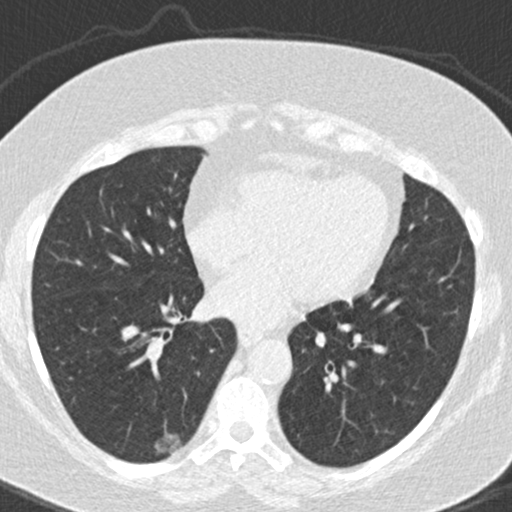
Low-dose screening chest CT, axial slice; baseline annual screen; lung window (W 1500 / L -600 HU); 2 mm slice thickness; standard (soft-tissue) reconstruction kernel (B30f); 120 kVp; slice 106 of 177 in the series; 512 × 512 image matrix, field of view 300 × 300 mm. Female participant, aged 63 years at enrolment. Former smoker at enrolment.
• Lesion marked by an expert reader, bounding box [x1, y1, x2, y2] px = [147, 425, 188, 462].
• Reader record for this screening exam (exam-level; its link to the box is not recorded): non-calcified nodule or mass ≥4 mm, right lower lobe, 16 × 10 mm, poorly defined margins, ground glass attenuation.
• Official screen result: positive, change unspecified: nodule(s) >= 4 mm or enlarging nodule(s), mass(es), or other non-specific abnormalities suspicious for lung cancer.
• Participant outcome: lung cancer diagnosed 246 days after this screen — bronchiolo-alveolar adenocarcinoma, NOS, right lower lobe, well differentiated (G1), stage IA (AJCC 6th edition), 12 mm at pathology.